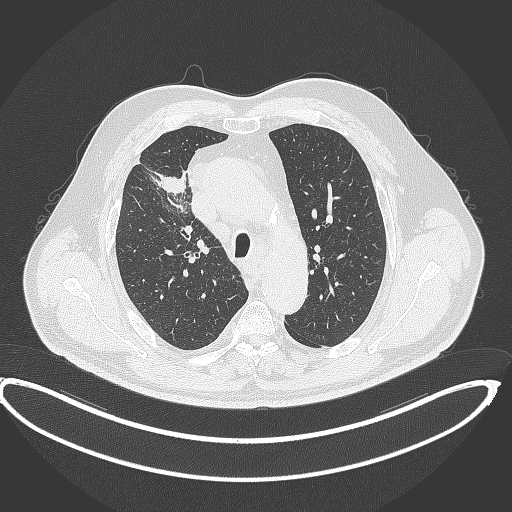
Chest CT, one axial slice; position 297 of 390 along the scan axis; lung window (W 1500 / L -600 HU); 1 mm slice thickness; 512 × 512 image matrix, field of view 448 × 448 mm. Male patient, age 62 years. Case-level facts recorded for this patient, not image findings: clinical TNM (as recorded): T1c N3 M1c.
Structures marked on this image (bounding box drawn by a radiologist):
- lung tumour (recorded histology: adenocarcinoma): bounding box [x1, y1, x2, y2] px = [156, 170, 187, 196]